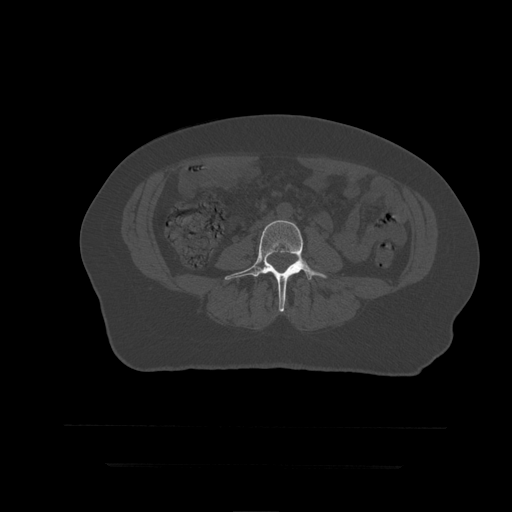
CT including the spine, one axial slice. Slice 99 of 399 in the series (ordered by position). 120 kVp. Bone window (W 1800 / L 400 HU). 1.25 mm slice thickness. 512 × 512 image matrix, field of view 450 × 450 mm. Patient age 41 years. From the clinical record (not read from this slice): primary cancer: breast.
Annotated regions visible in this slice (semi-automatically segmented with operator editing):
- L4 vertebra: bounding box <225,221,327,312> (left, top, right, bottom; pixels)